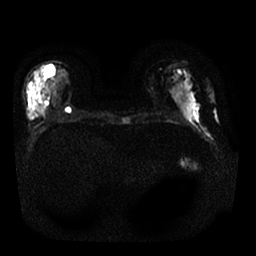
Breast MRI, one axial slice. Position 10 of 30 along the scan axis. Diffusion-weighted series; image 2 of 4 stored at this slice position (different b-values; order by instance number). 1.5 T. 256 × 256 image matrix. Female patient.
Annotated regions visible in this slice (outlined manually by an expert reader):
- tumour on diffusion-weighted imaging: bounding box [x1, y1, x2, y2] px = [28, 102, 48, 116]